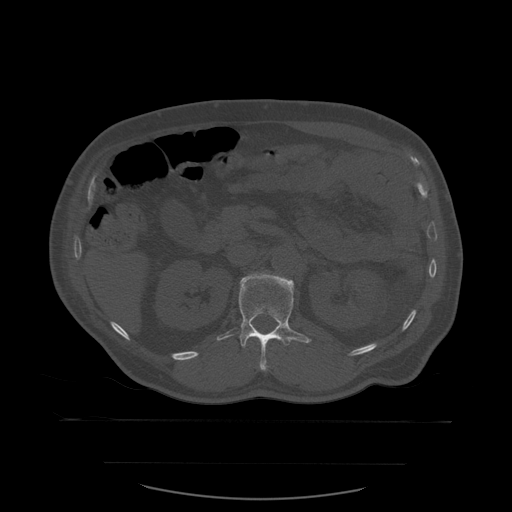
CT including the spine, one axial slice; slice 247 of 590 in the series (ordered by position); bone window (W 1800 / L 400 HU); 512 × 512 image matrix. Patient age 71 years. Case-level facts recorded for this patient, not image findings: primary cancer: lung; vertebrae with lytic lesions (as recorded): T1, T2, L5, S1.
Annotated regions visible in this slice (semi-automatic segmentation, software-assisted and operator-edited):
- L1 vertebra: bounding box [x1, y1, x2, y2] px = [217, 273, 312, 371]